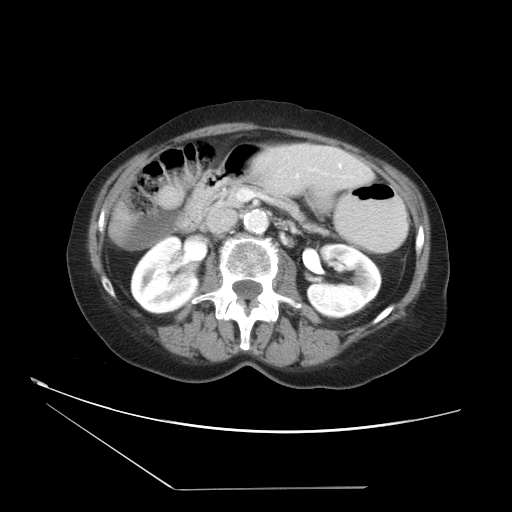
Contrast-enhanced abdominal CT, one axial slice. Position 13 of 36 along the scan axis. Intravenous contrast given. Soft-tissue window (W 400 / L 40 HU). 5 mm slice thickness. 512 × 512 image matrix, field of view 384 × 384 mm. Female patient, age 81 years. Case-level facts recorded for this patient, not image findings: diagnosis: colorectal cancer liver metastases, imaged before liver resection; multiple liver metastases: no; largest metastasis: 1.6 cm; disease in both lobes: no.
Outlined on this slice (manually delineated by an expert):
- liver: bounding box <158,144,374,210> (left, top, right, bottom; pixels)
- planned liver remnant (the part of the liver to remain after resection): <158,164,375,209>